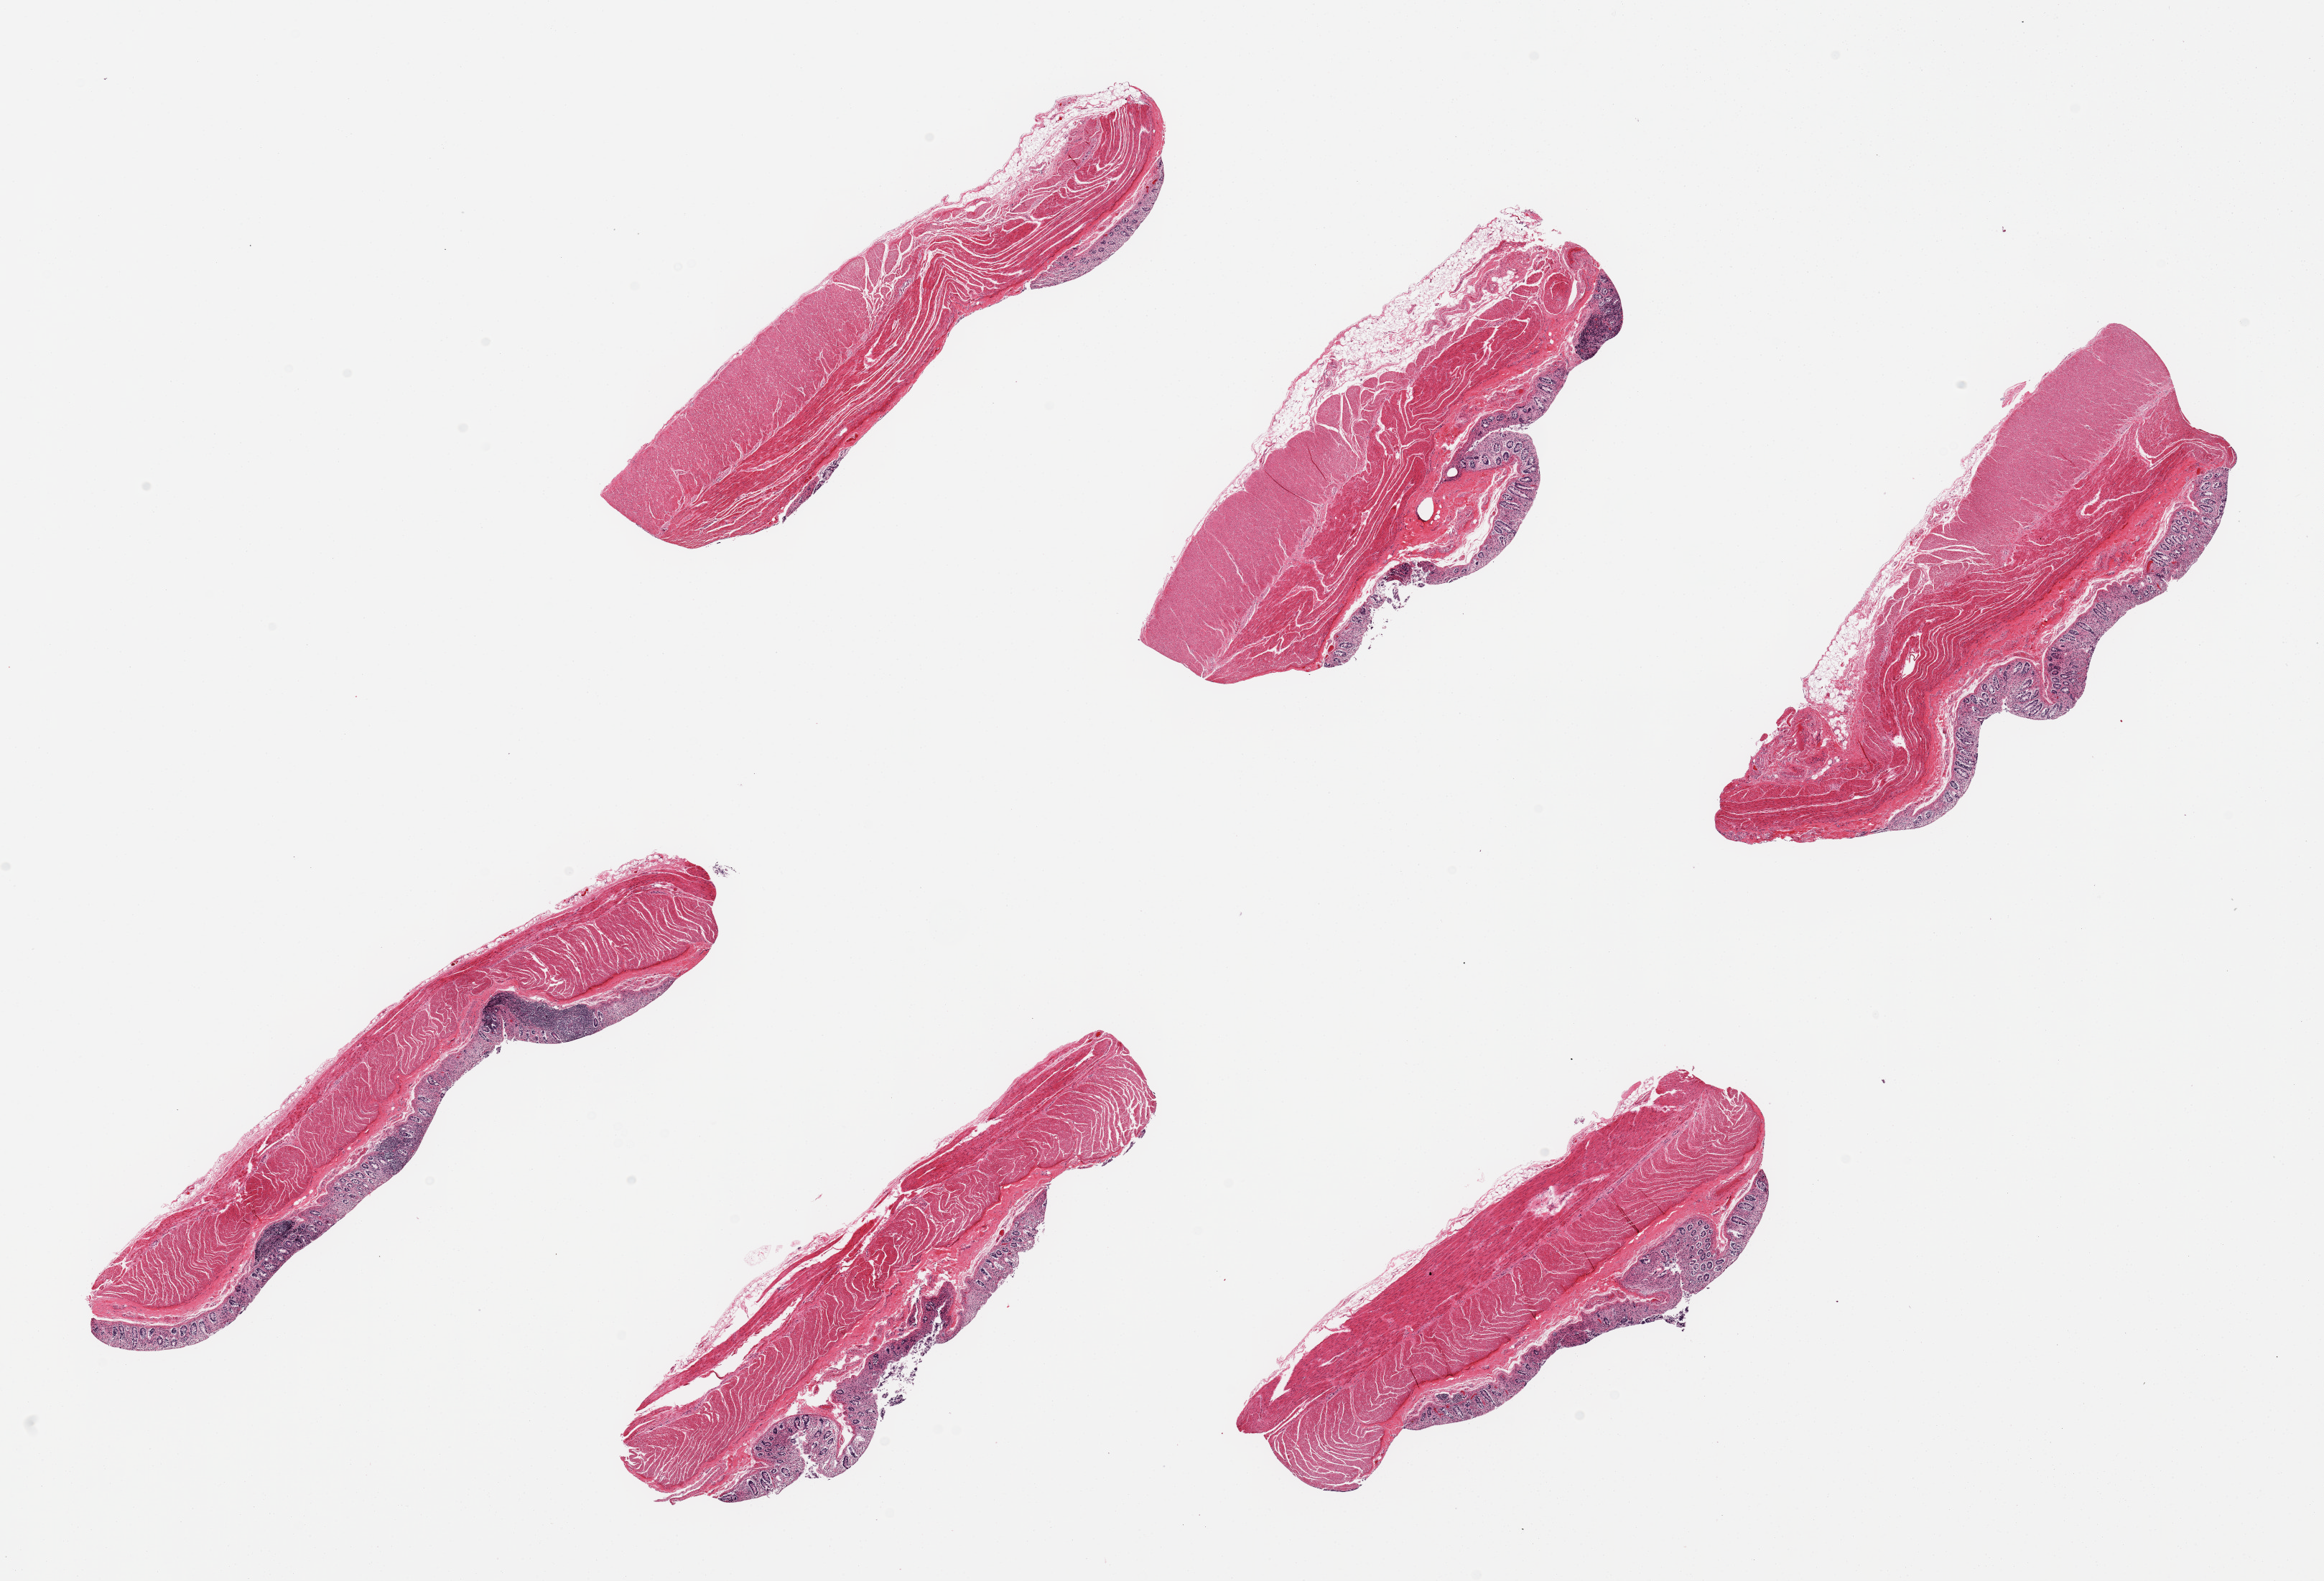
Digitized hematoxylin and eosin (H&E)-stained section, whole scanned area (about 25.6 x 17.4 mm, acquisition: 20x scan) shown as a low-resolution overview, PAXgene-fixed paraffin-embedded (PFPE) section, target tissue: transverse colon, donor tissue sample.
Review note (as recorded): 6 pieces; moderate to severe mucosal autolysis, muscularis.